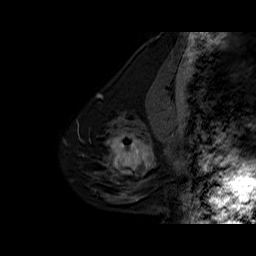
Breast MRI (dynamic contrast-enhanced), one sagittal slice; slice 17 of 60 in the series (ordered by position); dynamic contrast-enhanced series, time point 2 of 6 at this slice position (early post-contrast); 1.5 T; TE 6.3 ms, TR 32.5 ms; 256 × 256 image matrix. Female patient. From the clinical record (not read from this slice): setting: breast cancer imaged before/during neoadjuvant chemotherapy; receptor status: triple-negative.
Structures marked on this image (semi-automatic segmentation, software-assisted and operator-edited):
- analysis volume of interest (the breast-tissue region the enhancement analysis was run in; not a lesion): bounding box [x1, y1, x2, y2] px = [102, 127, 162, 186]
- tumour enhancement mask (voxels above the 100 % enhancement threshold inside the analysis volume of interest): [107, 133, 154, 174]